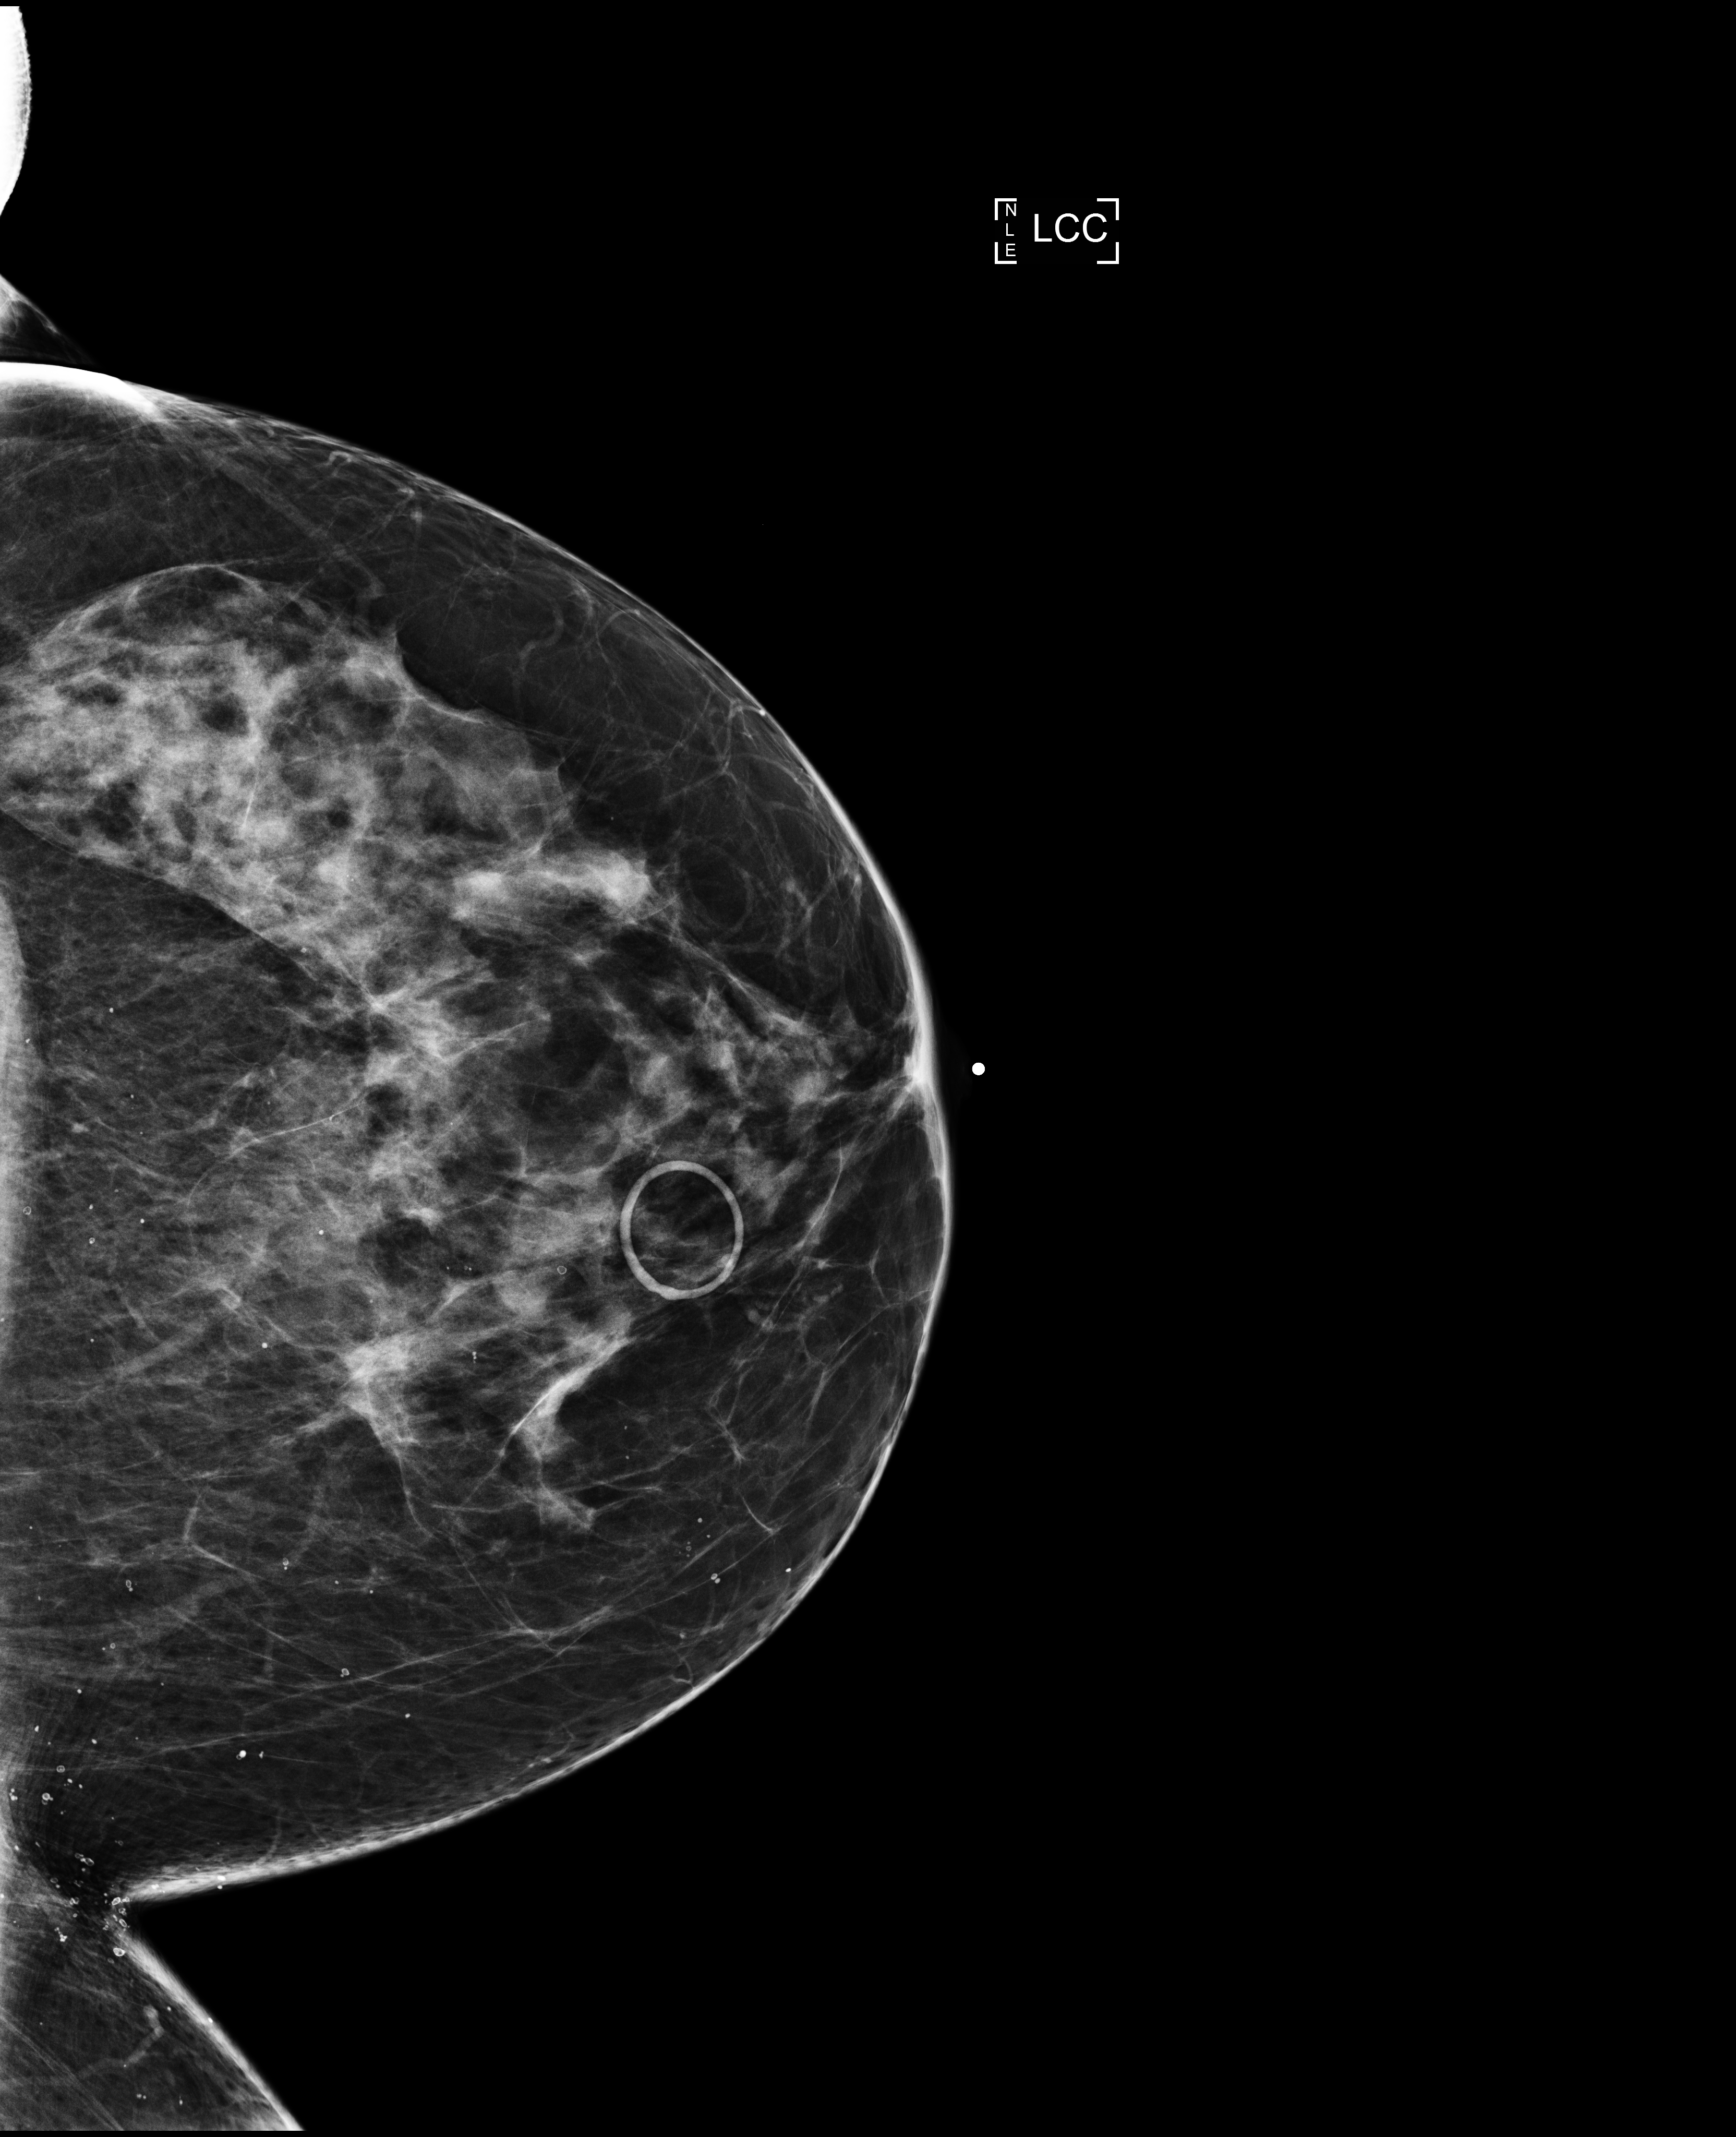
Screening examination, compressed breast thickness 69 mm, system: Selenia Dimensions. Patient: female, 61 years.
Image type: full-field digital mammogram. Breast: left. Projection: cranio-caudal projection.